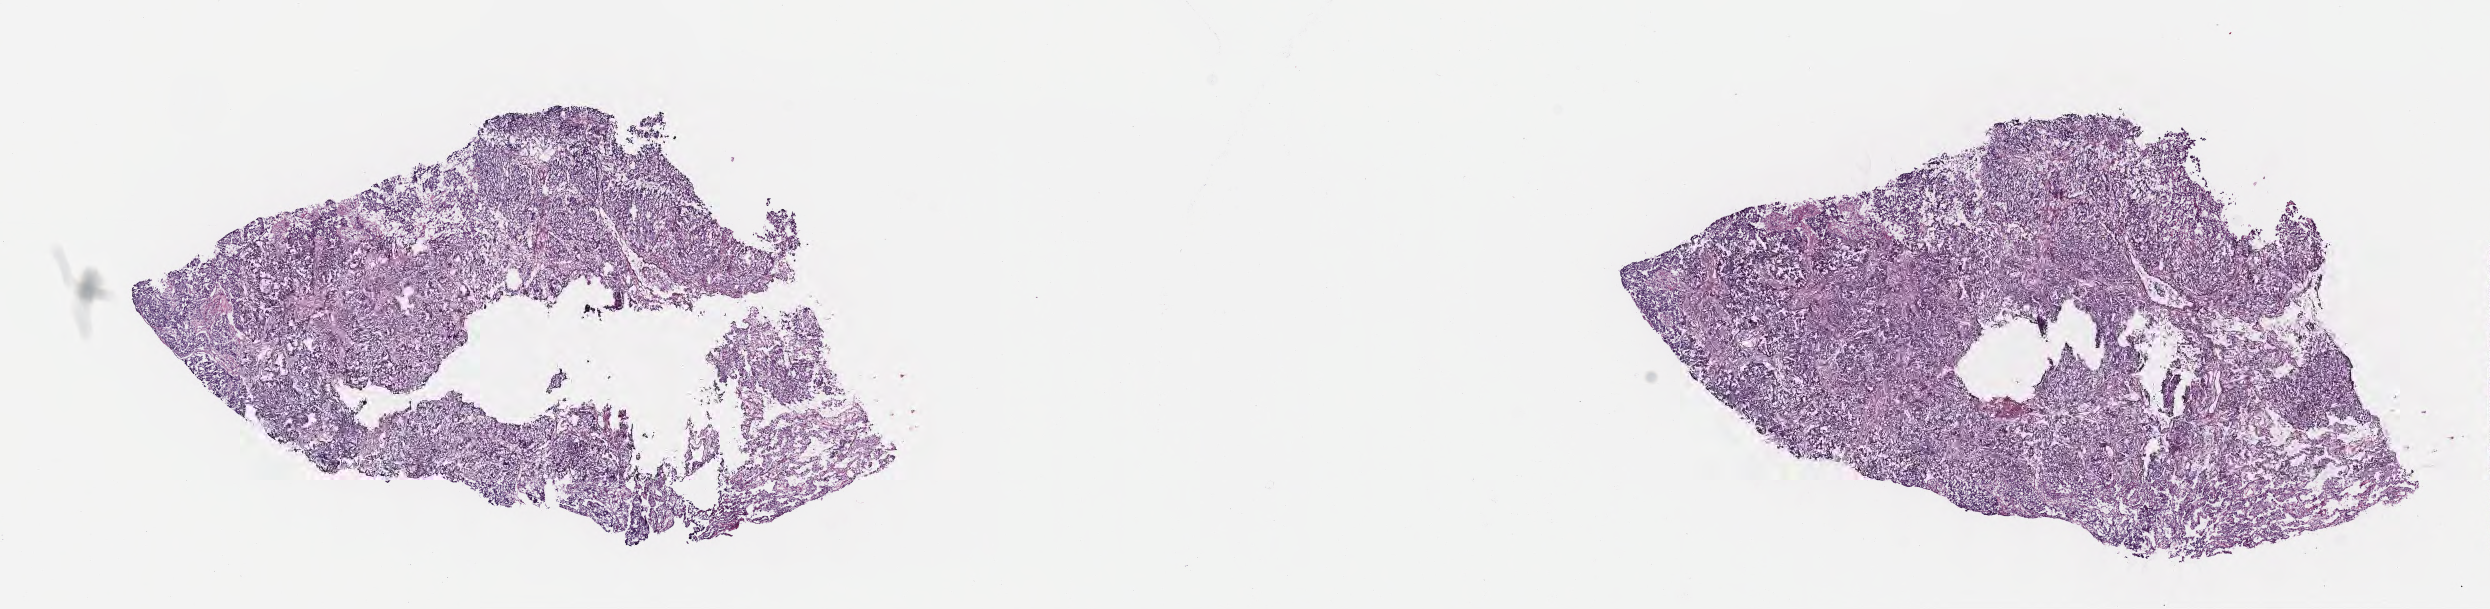
Haematoxylin and eosin whole-slide image — a low-resolution overview of the entire scanned area, about 20.1 x 4.9 mm; frozen section; specimen: primary tumor; site: upper lobe of left lung. Patient male; 65 years old. Composition of this section per pathologist review: tumor cells 70%, tumor nuclei 80%, stromal cells 20%, necrosis 0%, normal cells 10%. Infiltration values recorded for this section: lymphocyte infiltration 50%, monocyte infiltration 50%, neutrophil infiltration 0%.
- section: top of the tissue portion
- histologic diagnosis: Acinar cell carcinoma
- AJCC pathologic stage: Stage IIIA